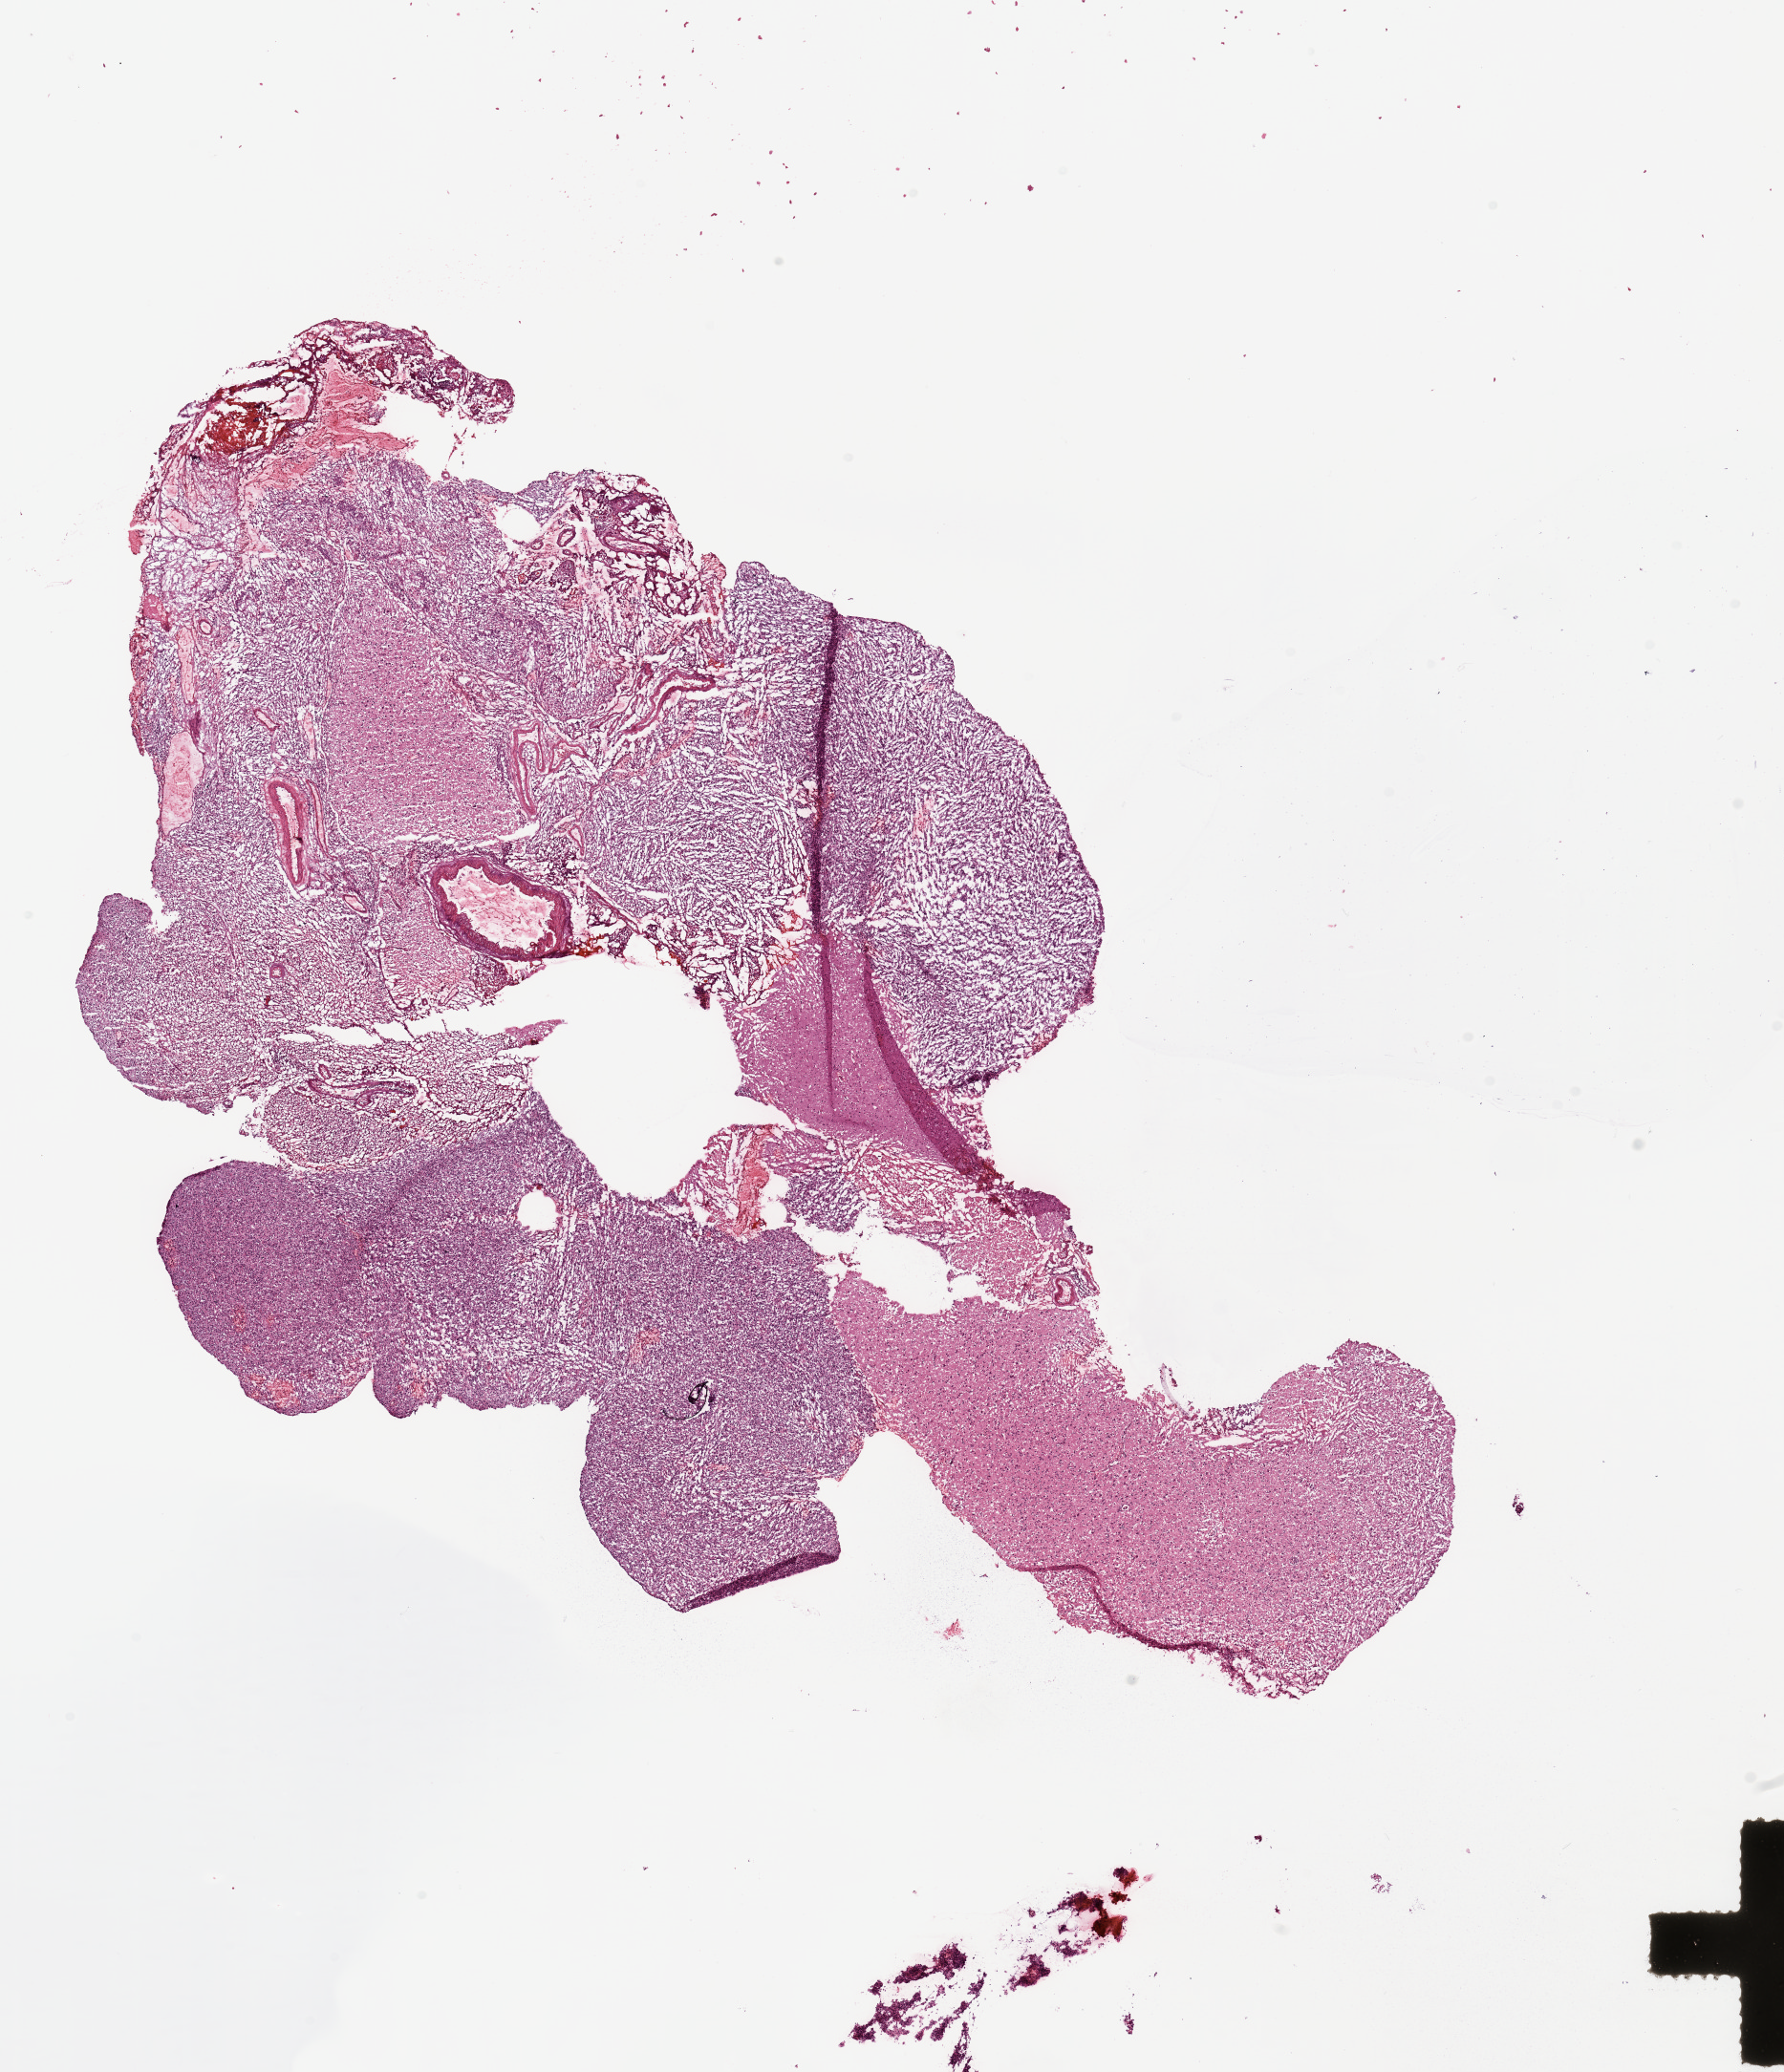
H&E whole-slide image — whole scanned area (about 14.8 x 17.2 mm, slide scanned at 20x) shown as a low-resolution overview. Tumour tissue sample, brain. Patient: male, age 60 years.
• primary tumour site (as recorded): parietal lobe
• patient diagnosis (cohort enrolment): glioblastoma multiforme (brain)